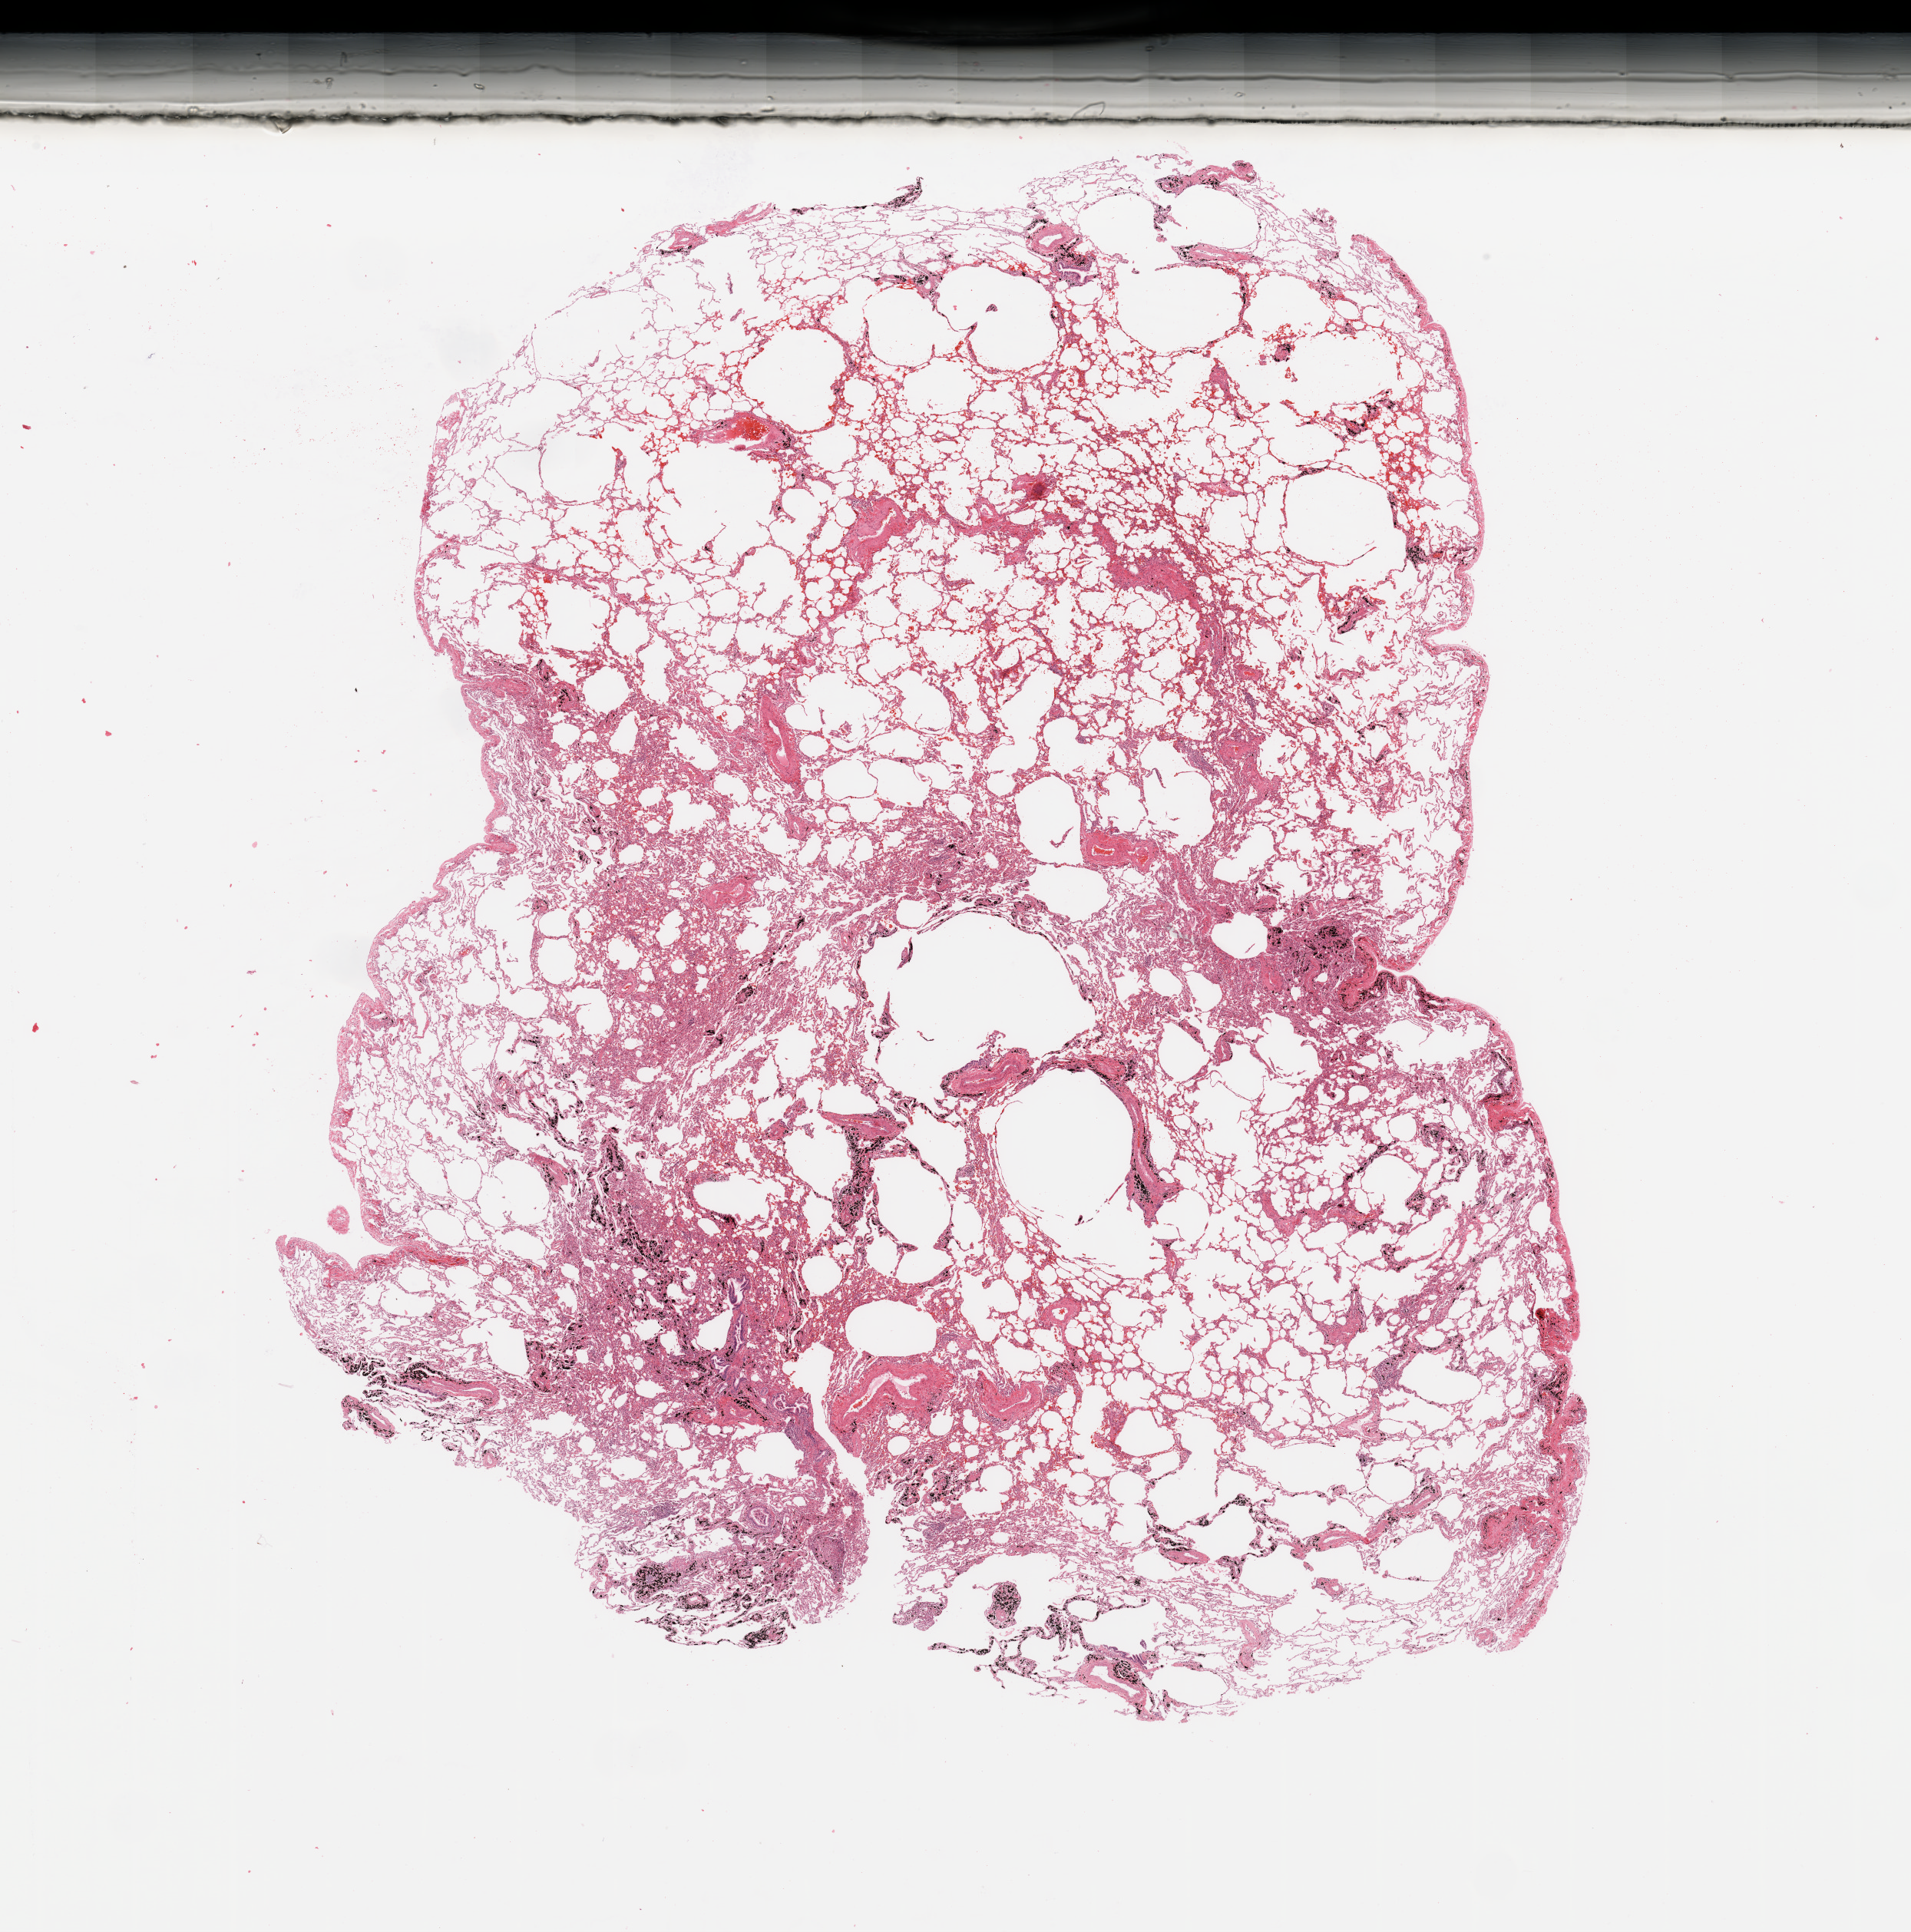
Whole-slide histology image, Hematoxylin and eosin (H&E) stained — shown as a low-resolution overview of the whole scanned area (about 19.7 x 19.9 mm, slide scanned at 20x), normal (non-tumour) tissue sample, sampled site: lung. 54-year-old male patient.
• this section: normal (non-tumour) tissue from the same patient
• patient diagnosis: Adenocarcinoma, NOS